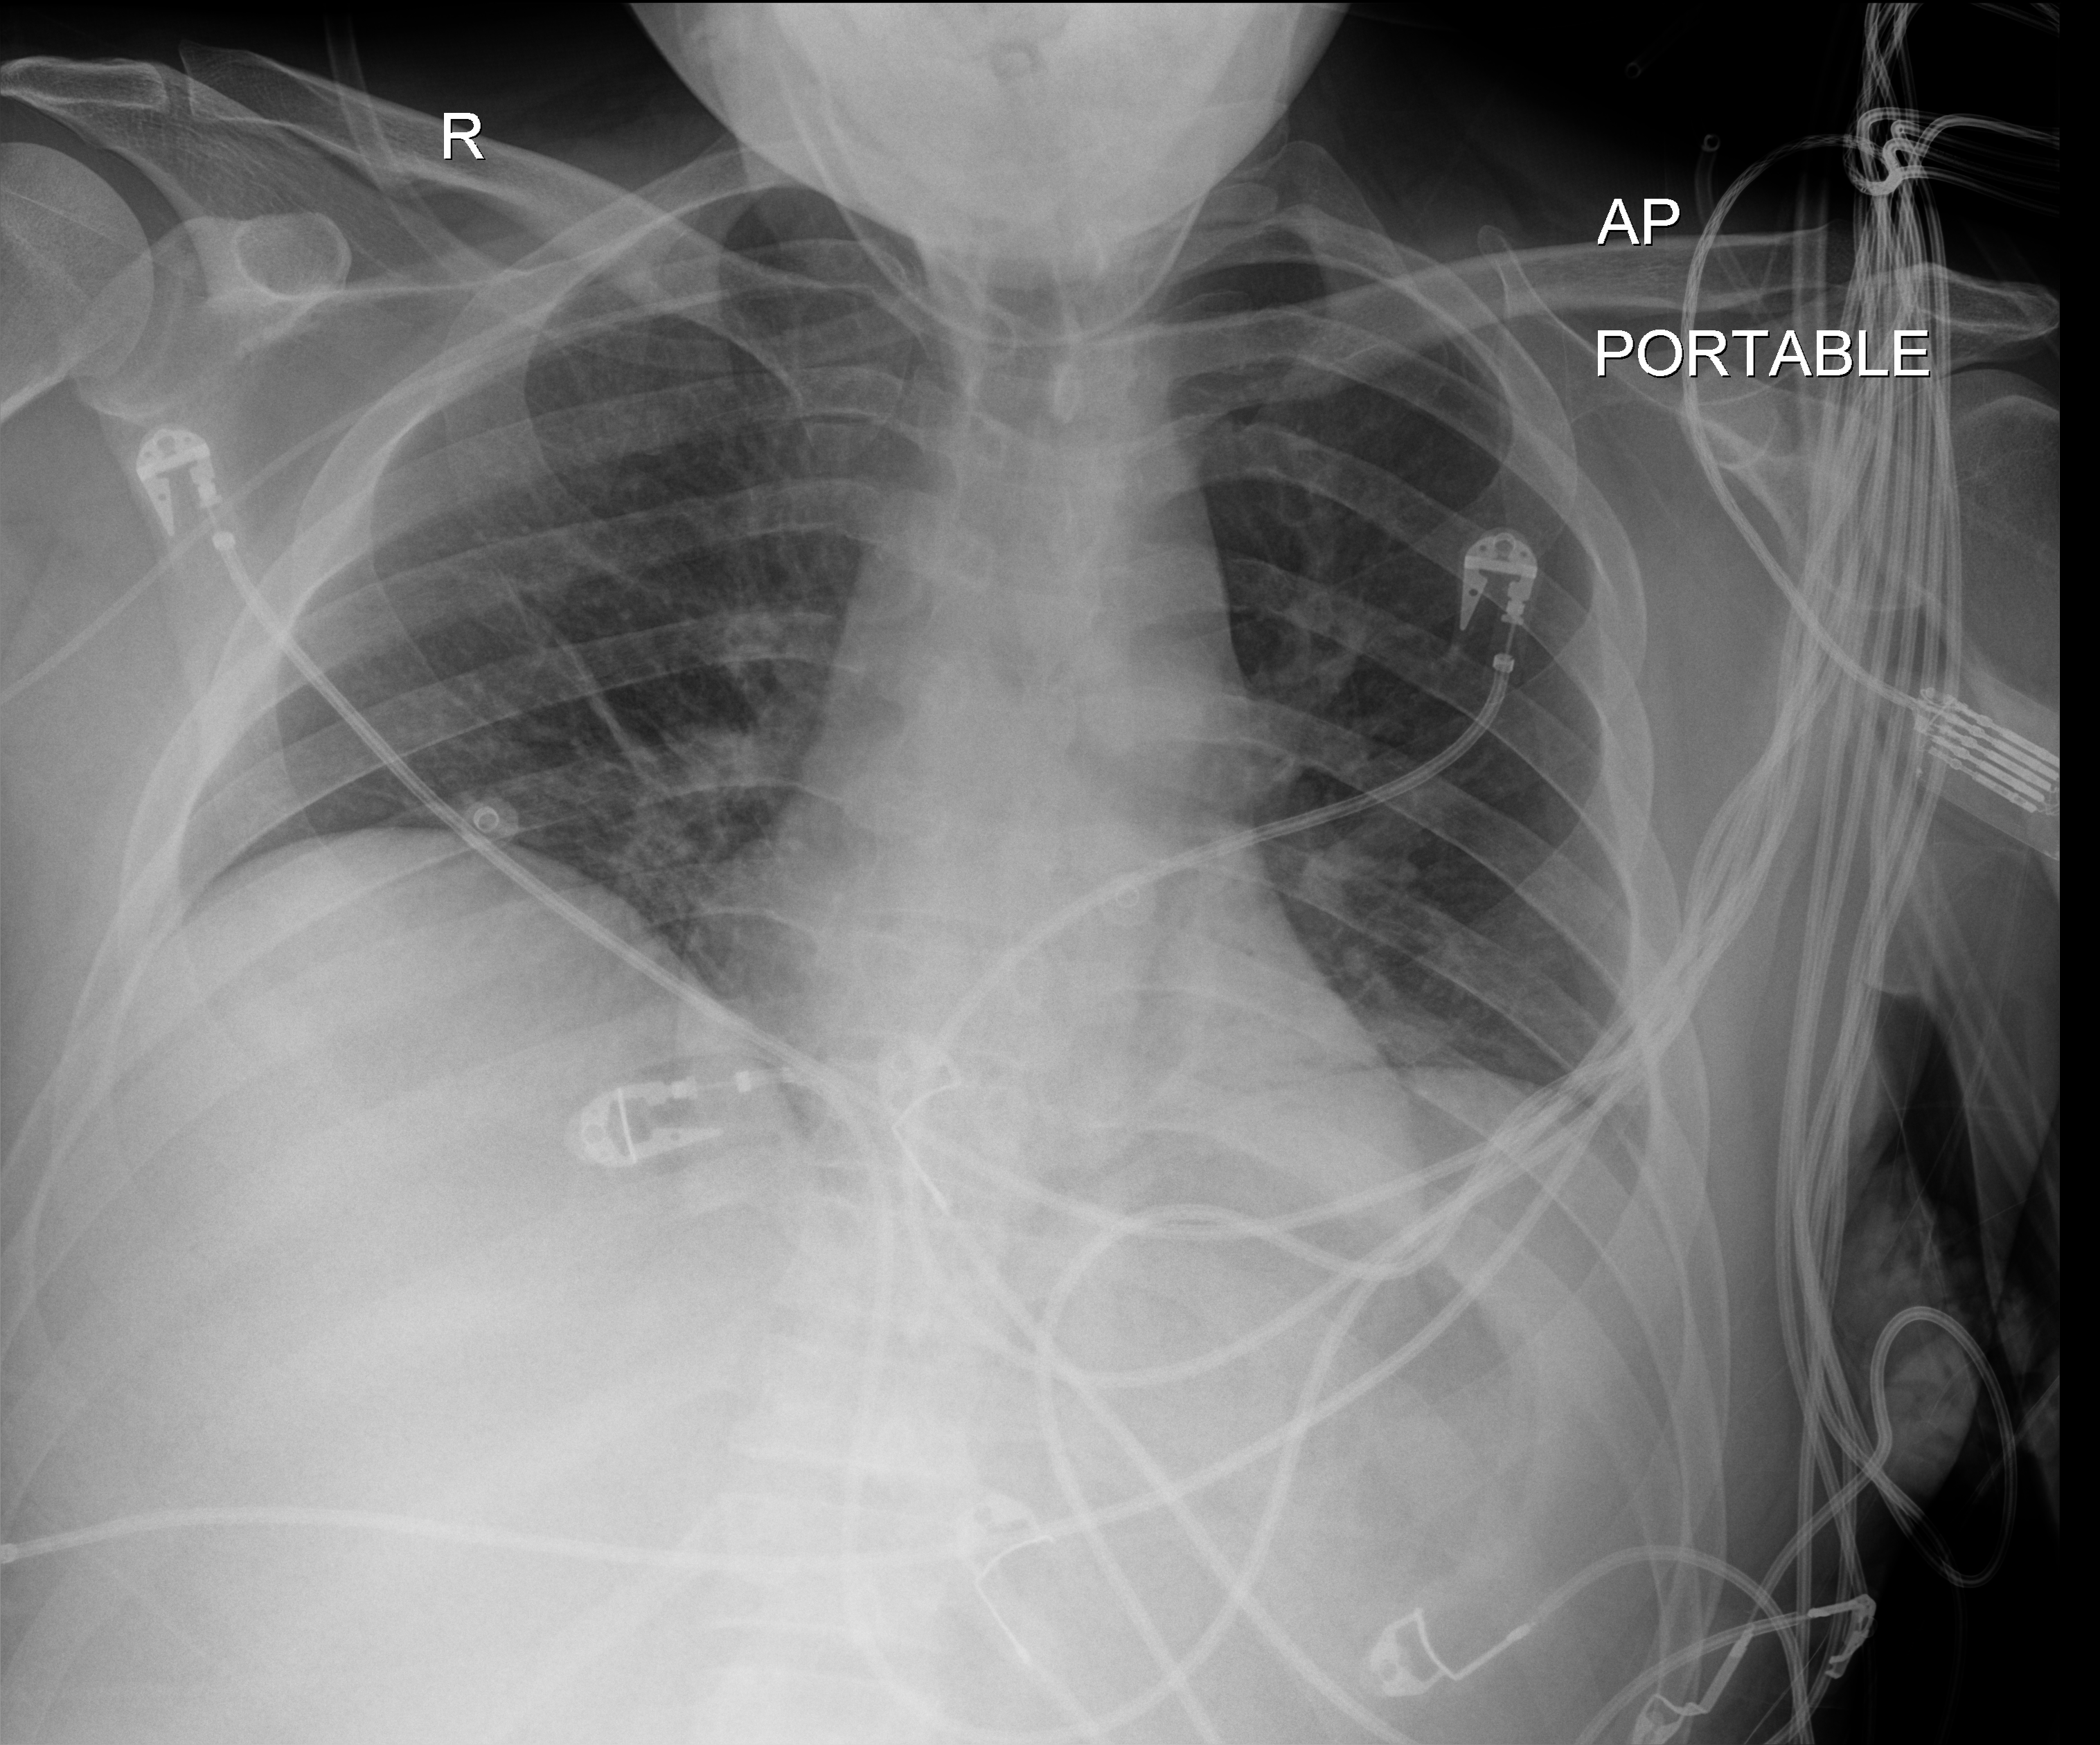
Portable chest radiograph, anteroposterior (AP) projection. Patient hospitalised with COVID-19; male, aged 18–59 years.
Hospital-stay facts (about this admission, not read from this image; timing relative to this image not recorded): chronic kidney disease (admission record): no; admitted to intensive care during this hospital stay: yes.